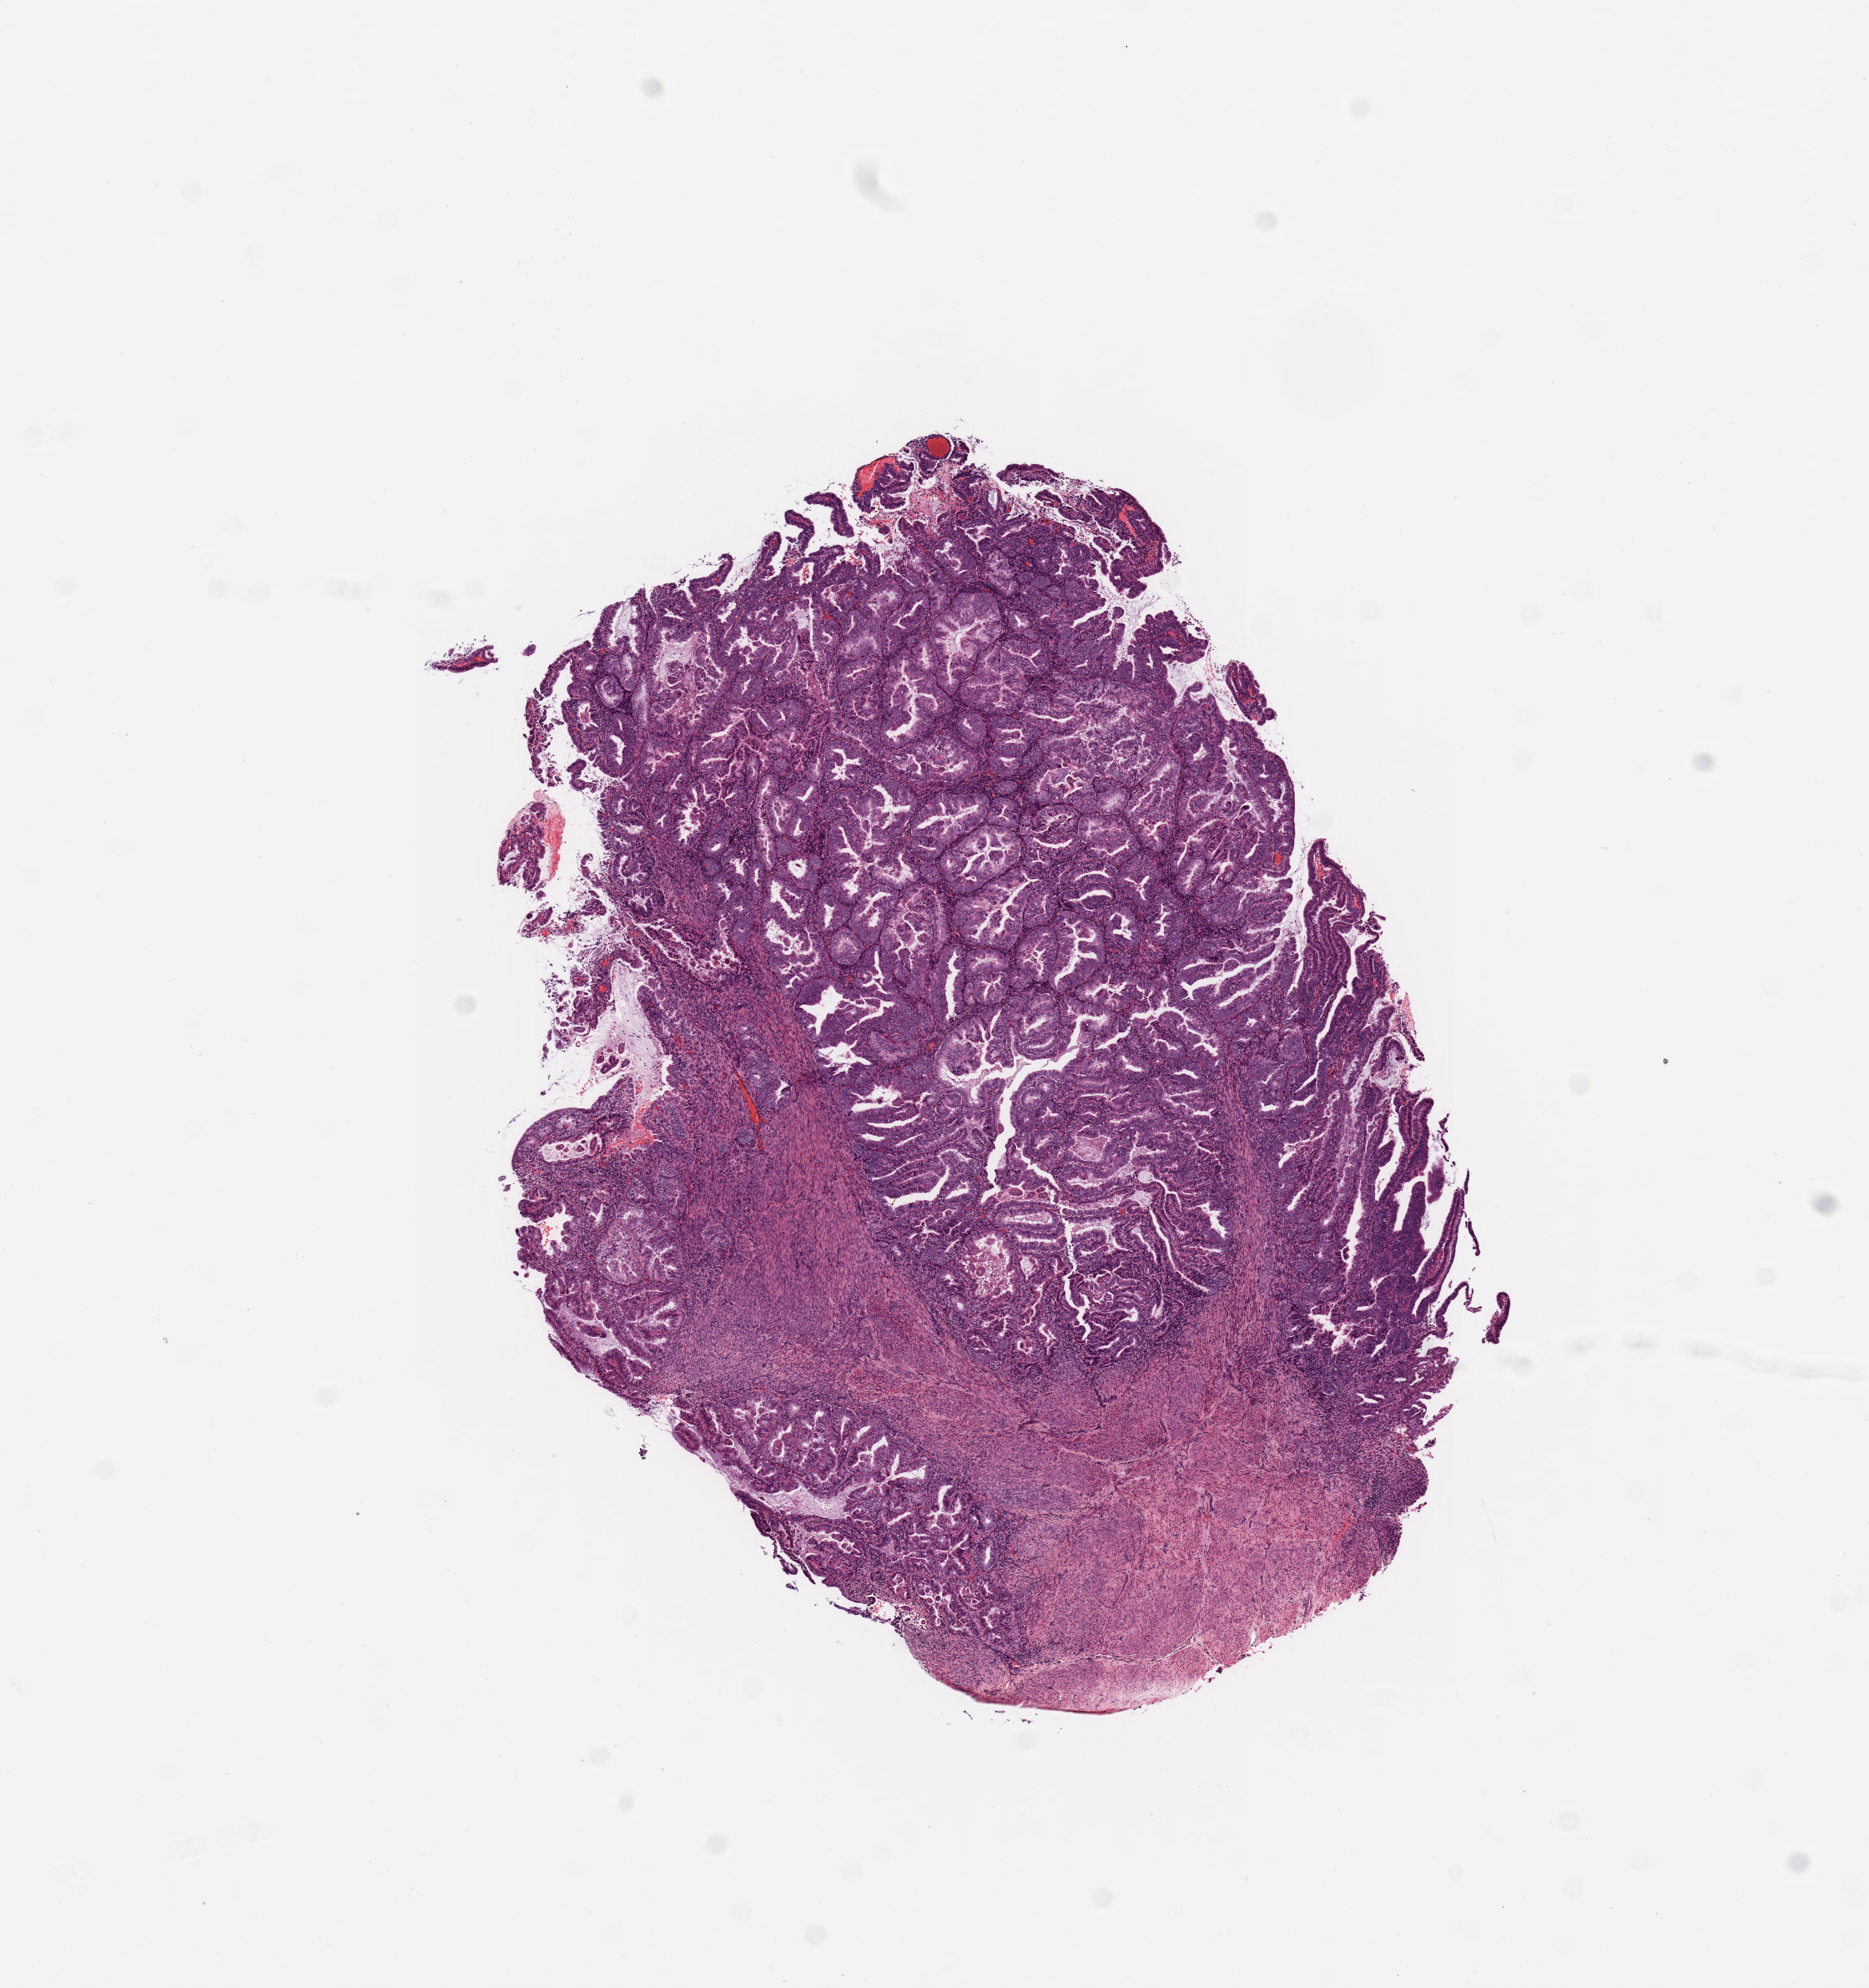
Digitized H&E-stained tissue section (whole slide), a low-resolution overview of the entire scanned area, about 8.9 x 9.4 mm (acquisition: 20x scan), tumour tissue sample, uterus. 60-year-old female patient. Histologic grade: G1 (well differentiated).
- AJCC pathologic stage: I
- diagnosis: Endometrioid adenocarcinoma, NOS